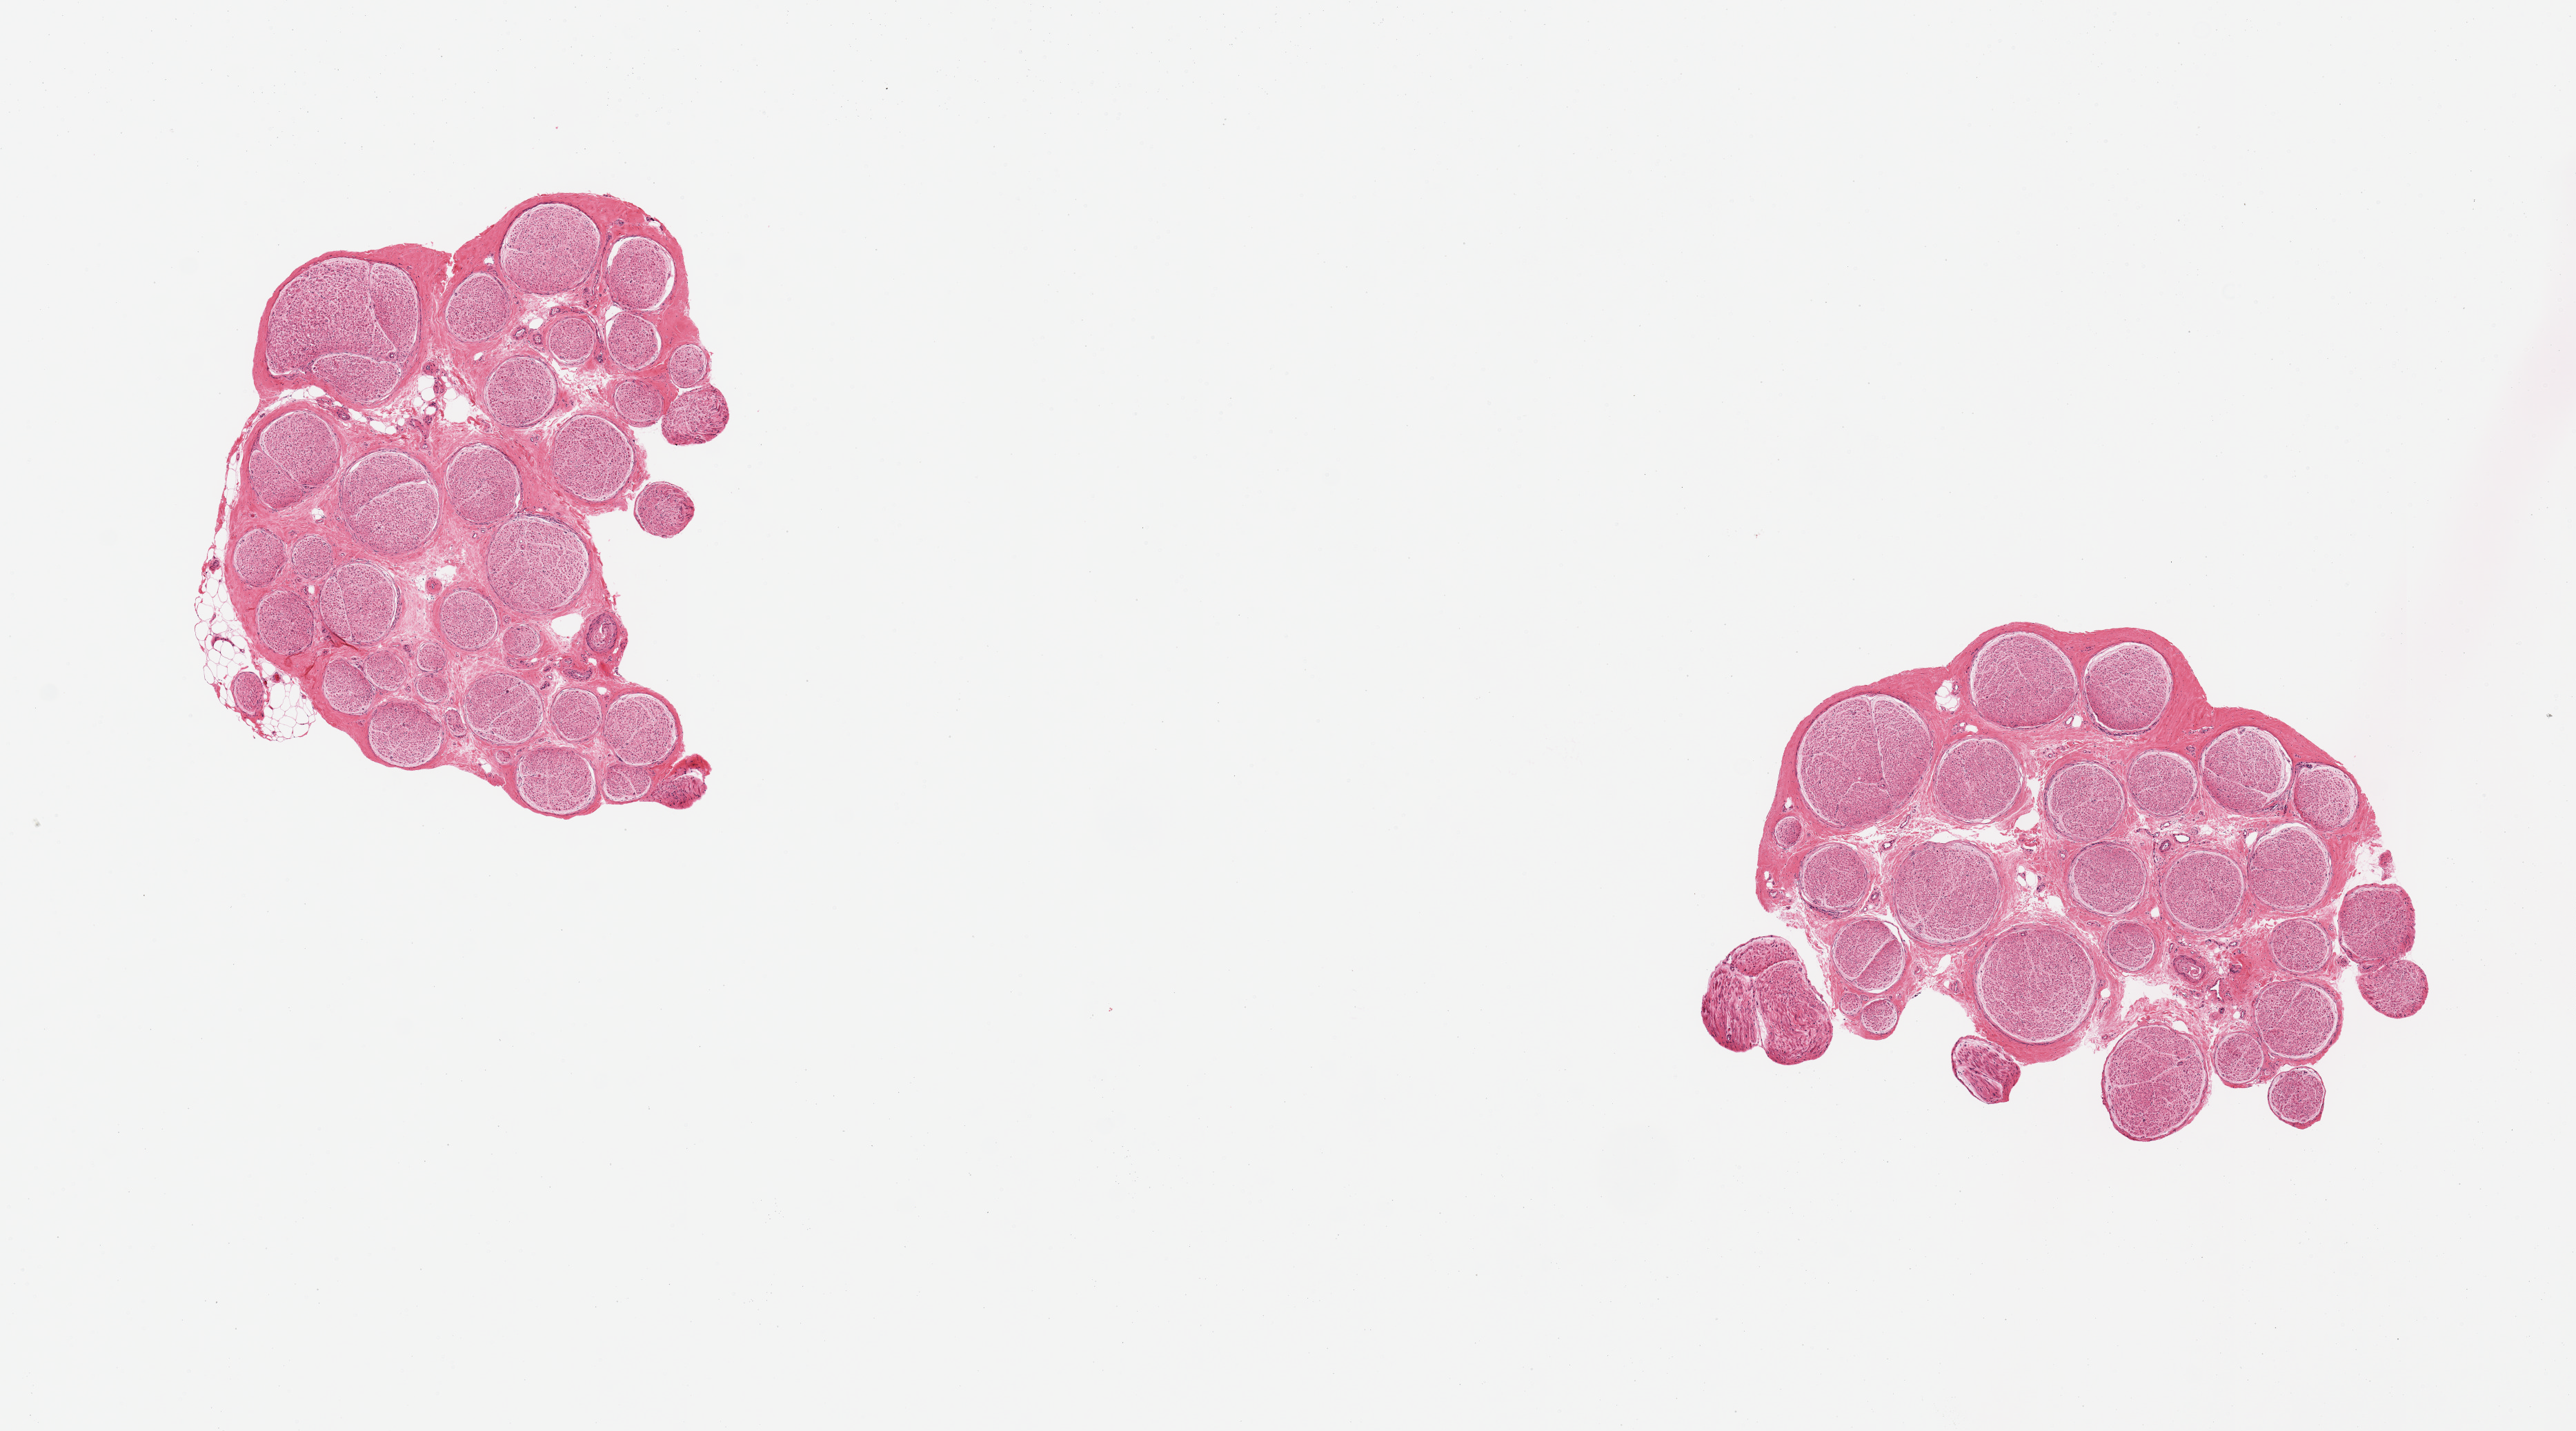
Whole-slide image, hematoxylin and eosin (H&E) stain — low-resolution overview of the scanned area, about 14.8 x 8.2 mm (acquisition: 20x scan); PAXgene-fixed, paraffin-embedded tissue; section of tibial nerve (target tissue); tissue donor sample.
Pathologist's review note for this sample: 2 pieces, no adherent fat; excellent specimens.